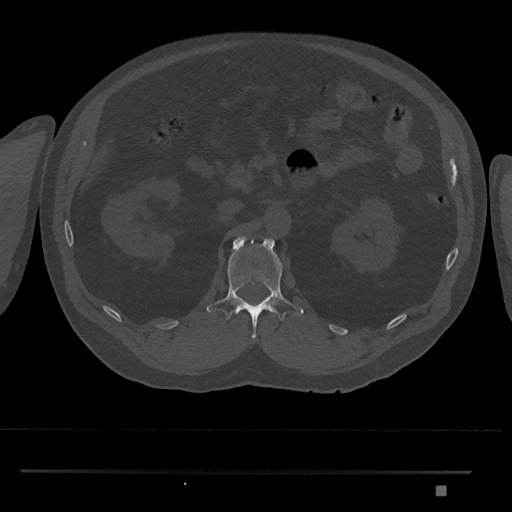
CT including the spine, one axial slice. Position 821 of 1134 along the scan axis. Reconstruction kernel Br40s/3. 120 kVp. Bone window (W 1800 / L 400 HU). 0.5 mm slice thickness. 512 × 512 image matrix. Patient: male, 65 years. From the clinical record (not read from this slice): primary cancer: prostate.
Annotated regions visible in this slice (semi-automatically segmented with operator editing):
- L1 vertebra: bounding box <206,236,304,340> (left, top, right, bottom; pixels)